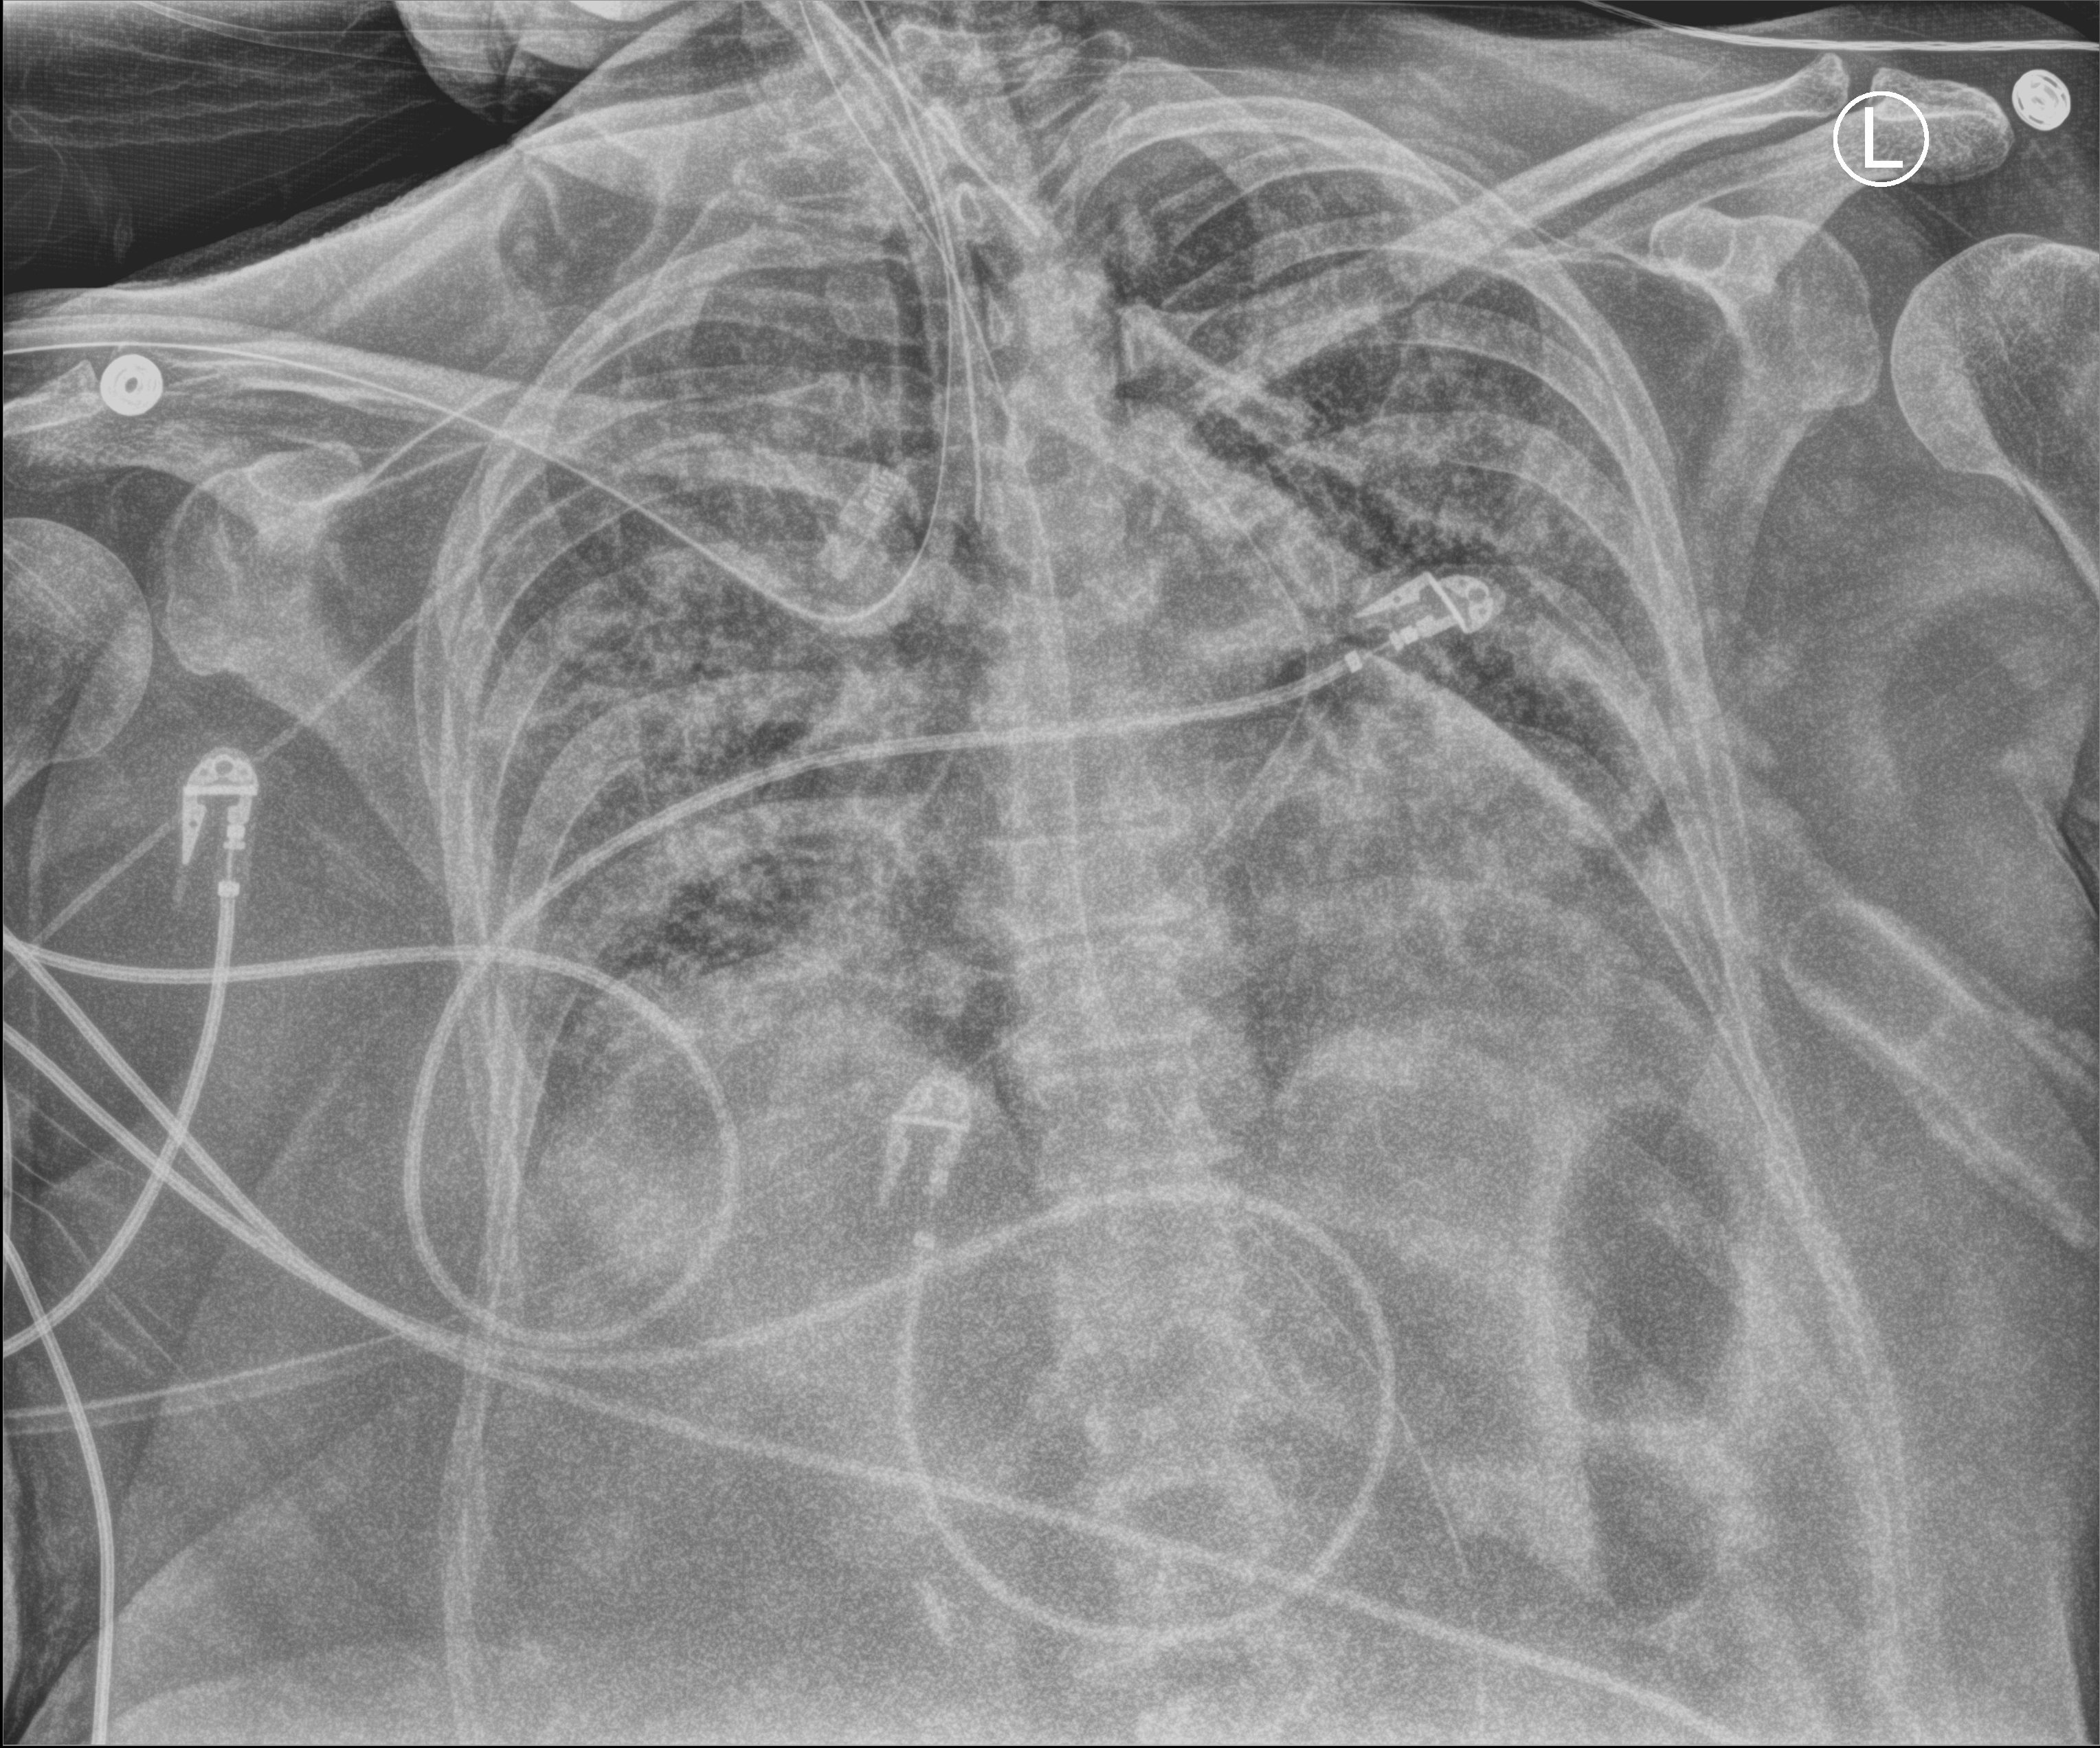
Portable chest radiograph; anteroposterior (AP) projection. Female patient hospitalised with COVID-19, age 60–74 years.
From the hospital-stay record, not from the radiograph (when in the stay this image was taken is not recorded):
- admitted to intensive care during this hospital stay: yes